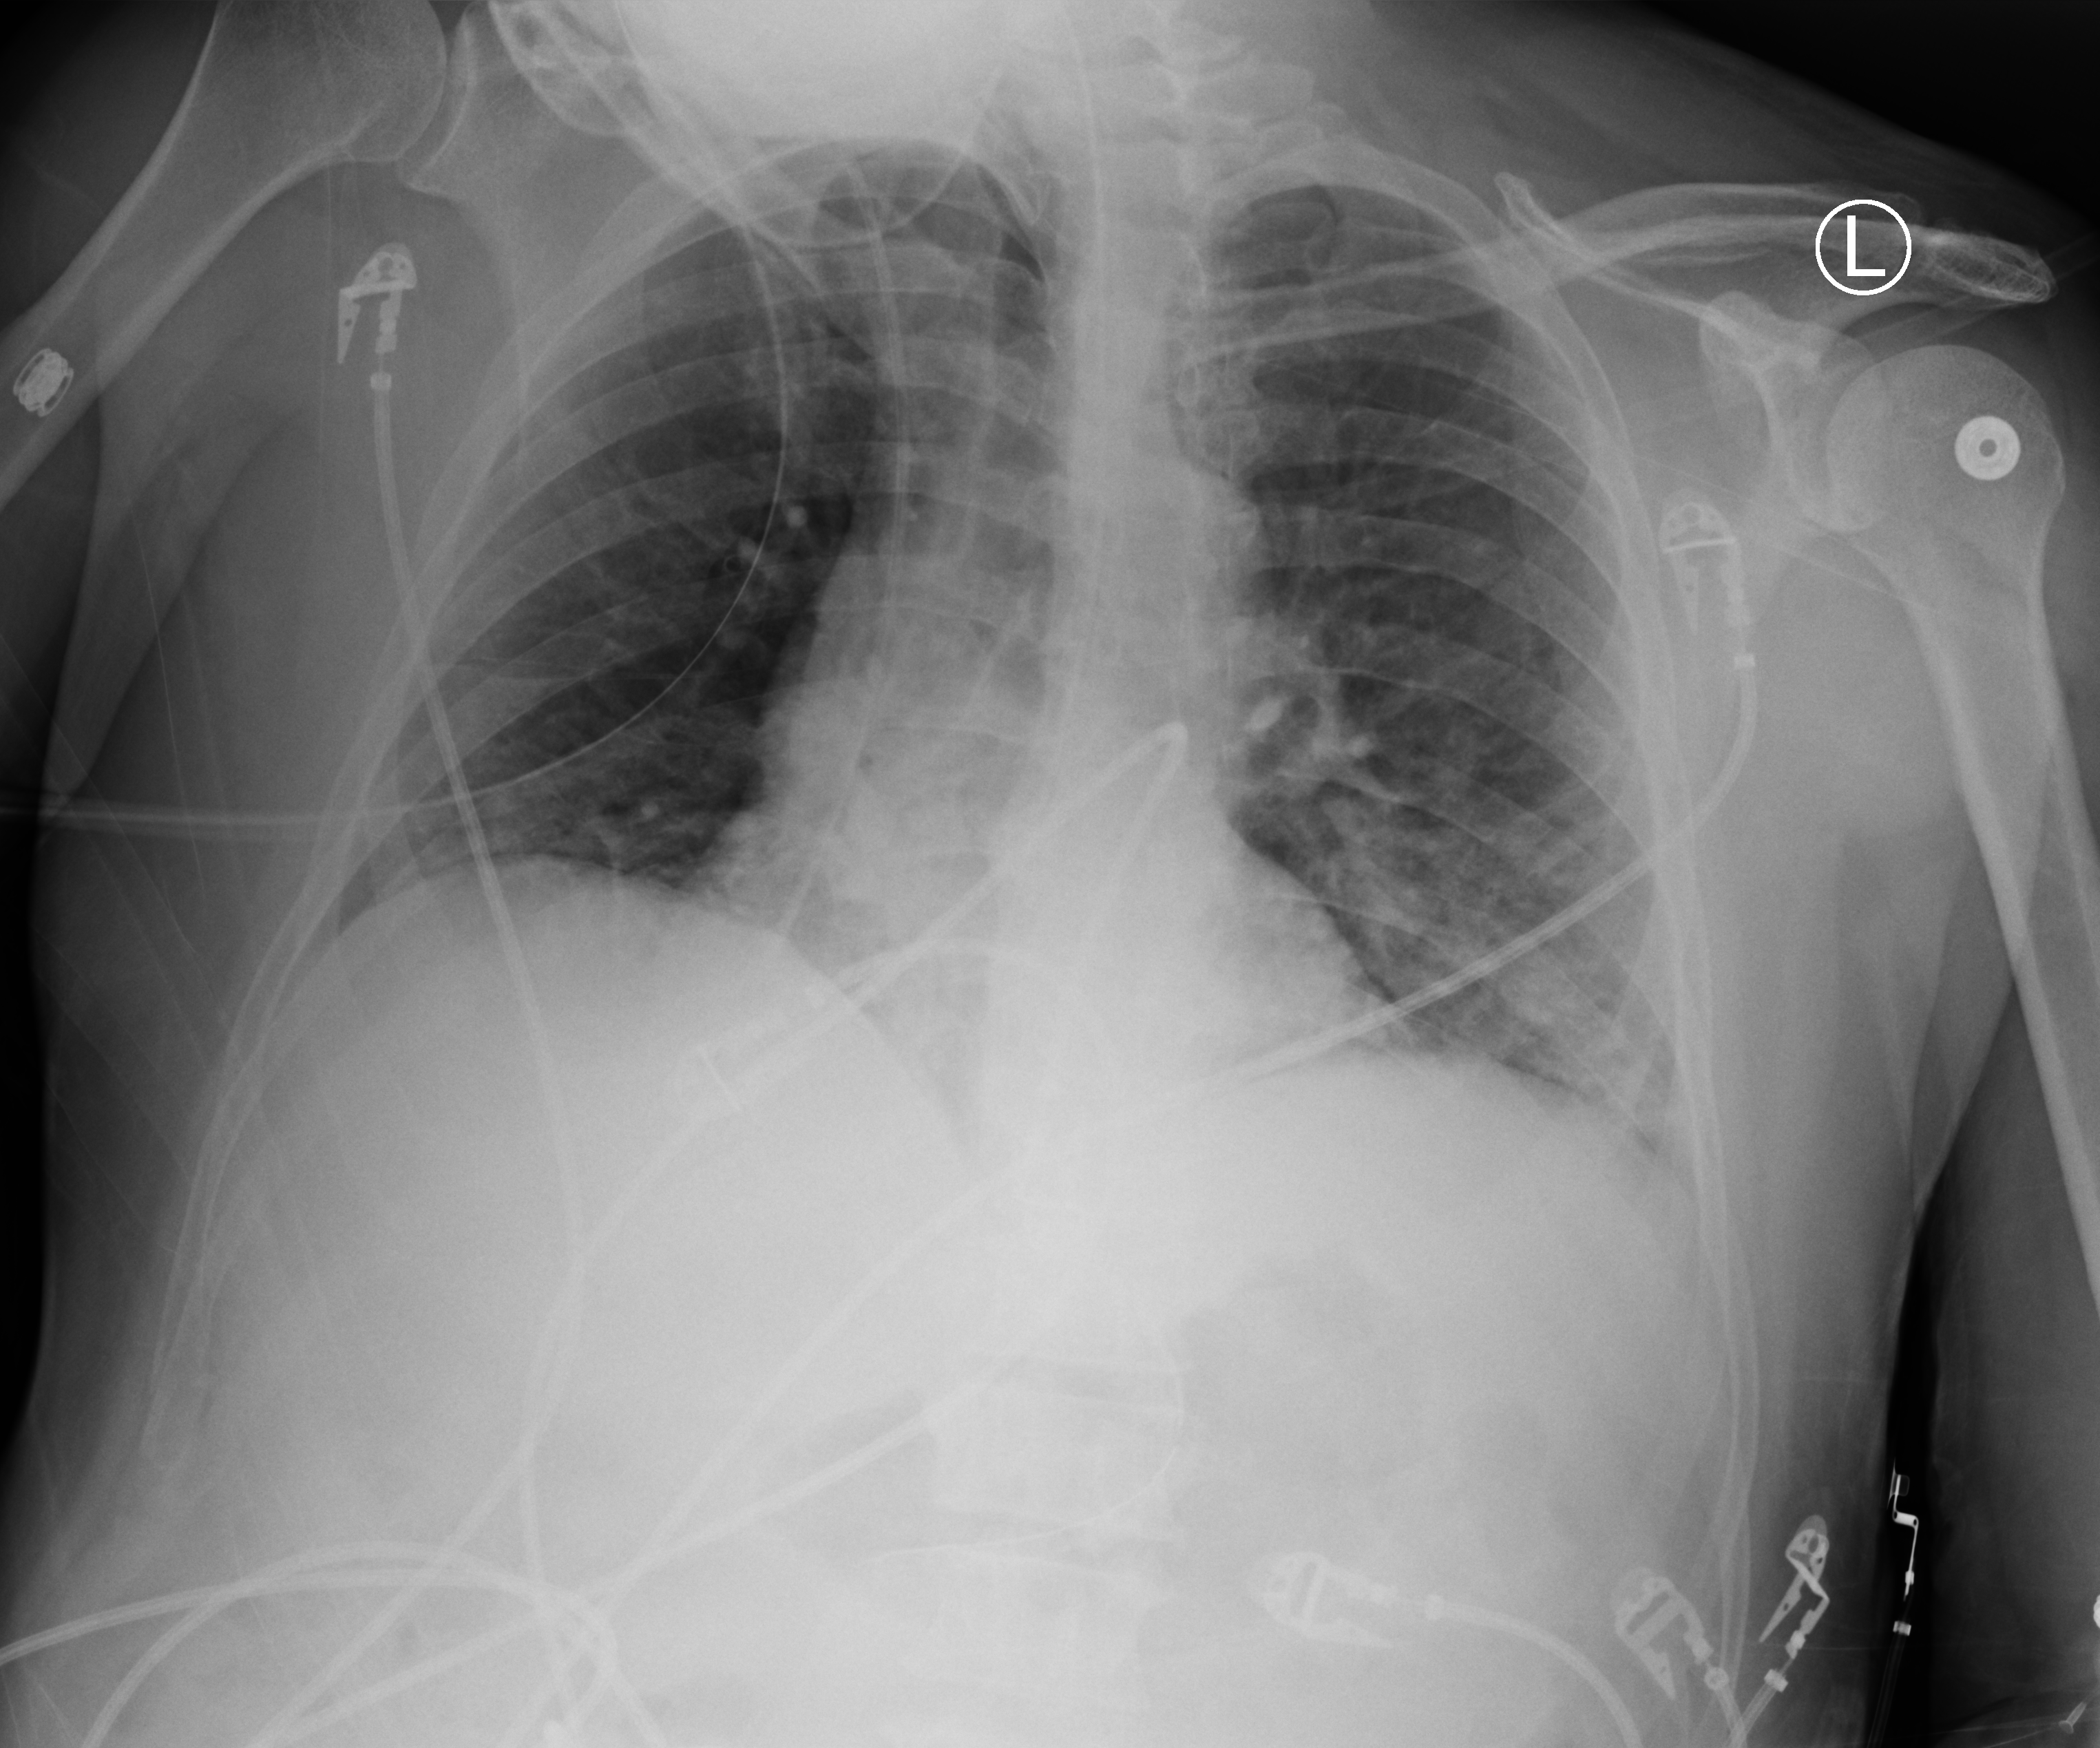
Portable chest radiograph, anteroposterior (AP) projection. Patient hospitalised with COVID-19; male, aged 18–59 years.
Hospital-stay facts (about this admission, not read from this image; timing relative to this image not recorded): mechanically ventilated during this hospital stay: yes; other chronic lung disease (admission record): no.